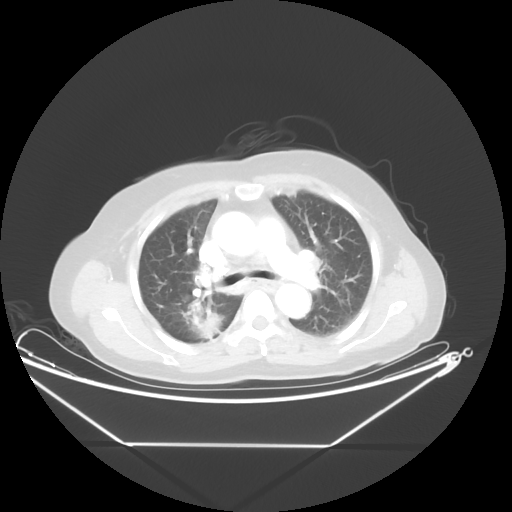
Chest CT, one axial slice; reconstruction kernel STANDARD; lung window (W 1500 / L -600 HU); 5 mm slice thickness; 512 × 512 image matrix, field of view 462 × 462 mm. Patient: female, 62 years. From the clinical record (not read from this slice): clinical TNM (as recorded): T1c N0 M0.
Outlined on this slice (rectangle marked by the reading radiologist):
- lung tumour (recorded histology: adenocarcinoma): bounding box <183,300,234,349> (left, top, right, bottom; pixels)